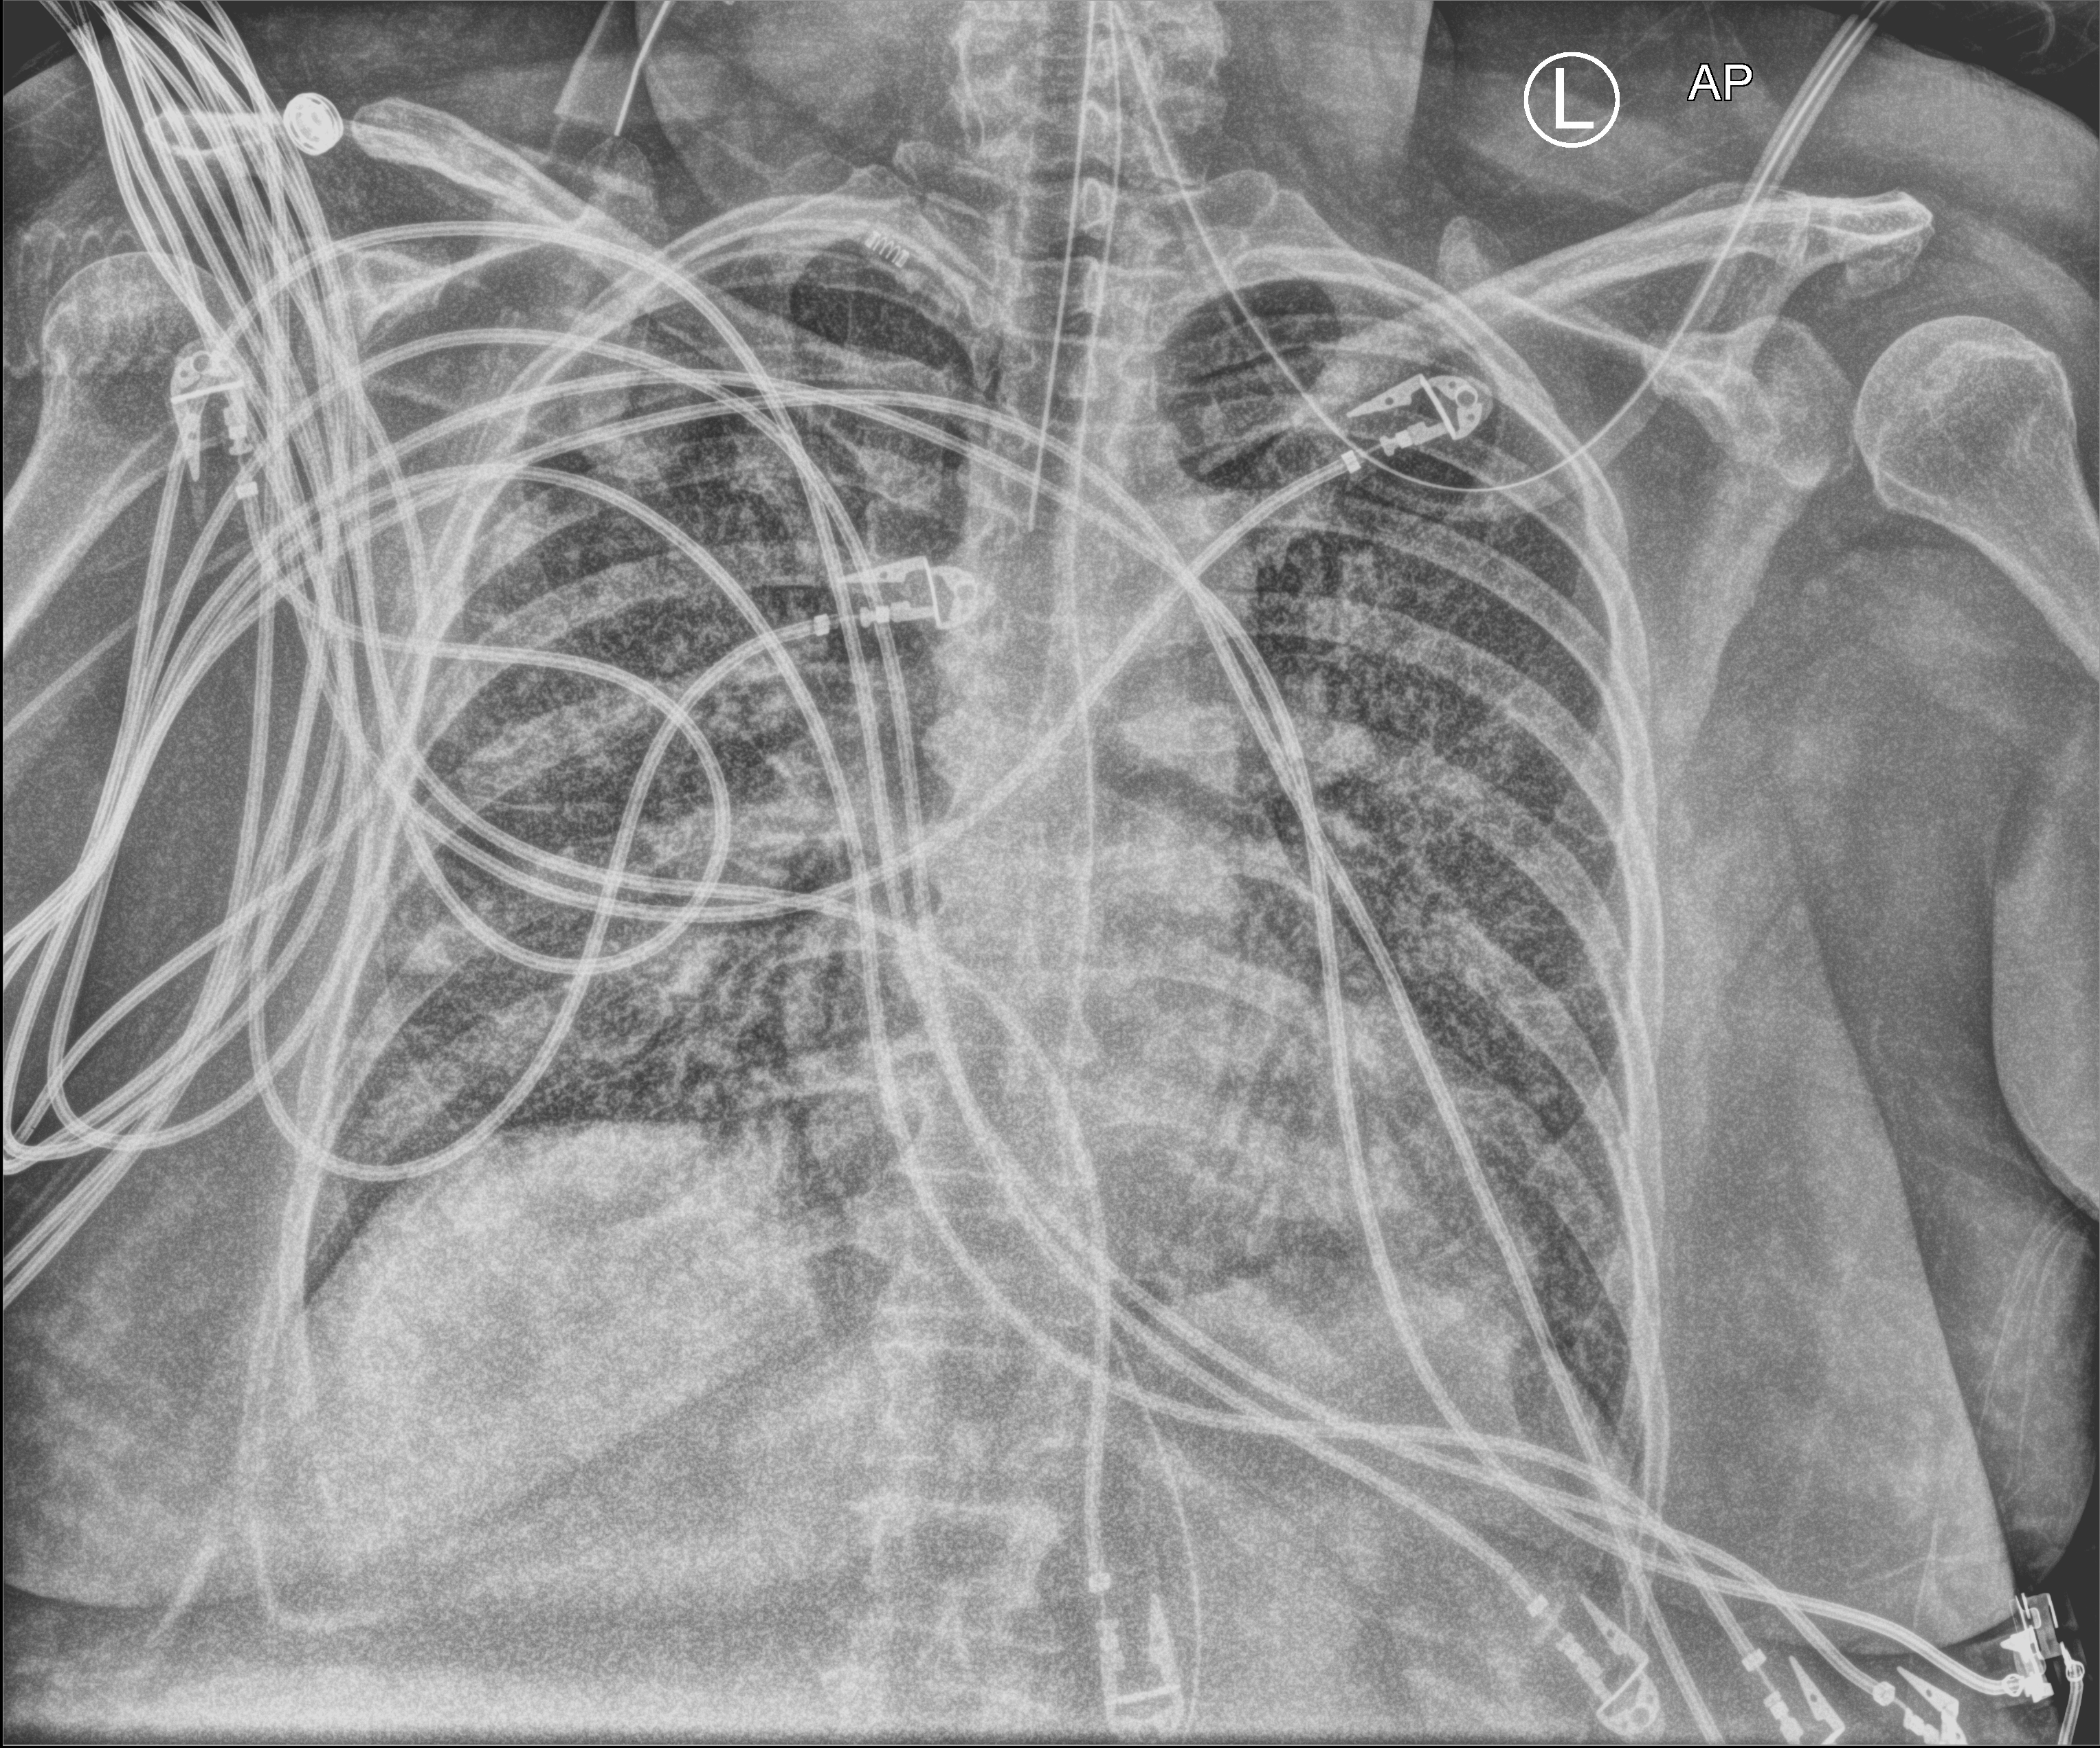
Chest X-ray (portable); anteroposterior (AP) projection. Patient hospitalised with COVID-19; female, aged 60–74 years.
Admission-level facts for this patient (not findings on this image; timing relative to this image not recorded): COPD (admission record): no.